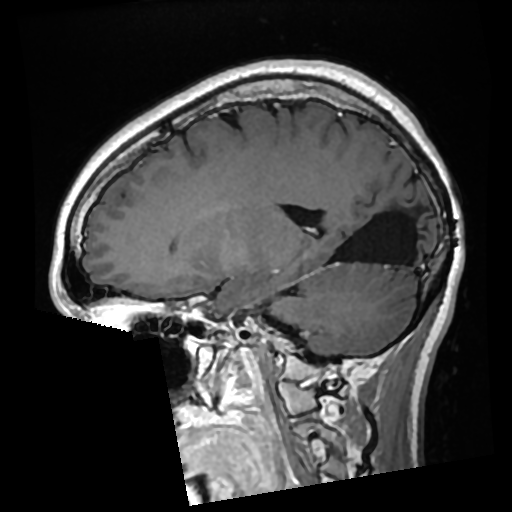
Brain MRI from a brain-tumour surgery series, one sagittal slice. Position 113 of 276 along the scan axis. T1-weighted post-contrast. 512 × 512 image matrix, field of view 250 × 250 mm. From the clinical record (not read from this slice): histopathology: Glioma with ependymal features; WHO grade: 2; tumour location: Left Parietal.
Annotated regions visible in this slice (manually delineated by an expert):
- previous resection cavity: box from (x=336, y=194) to (x=422, y=264) px